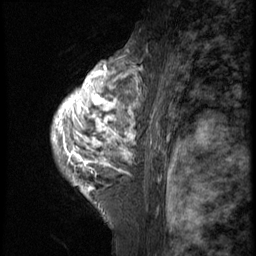
Breast MRI (dynamic contrast-enhanced), one sagittal slice. Slice 42 of 58 in the series (ordered by position). 3 images stored at this slice position (order not interpretable as contrast timing). 1.5 T. TE 4.2 ms, TR 9 ms. 2.5 mm slice thickness. 256 × 256 image matrix, field of view 180 × 180 mm. Patient: female, 50 years. Case-level facts recorded for this patient, not image findings: setting: breast cancer imaged before/during neoadjuvant chemotherapy; receptor status: triple-negative.
Structures marked on this image (semi-automatic segmentation, software-assisted and operator-edited):
- analysis volume of interest (the breast-tissue region the enhancement analysis was run in; not a lesion): bounding box (x1, y1, x2, y2) in pixels: (52, 48, 130, 214)
- tumour enhancement mask (voxels above the 140 % enhancement threshold inside the analysis volume of interest): (55, 59, 130, 193)